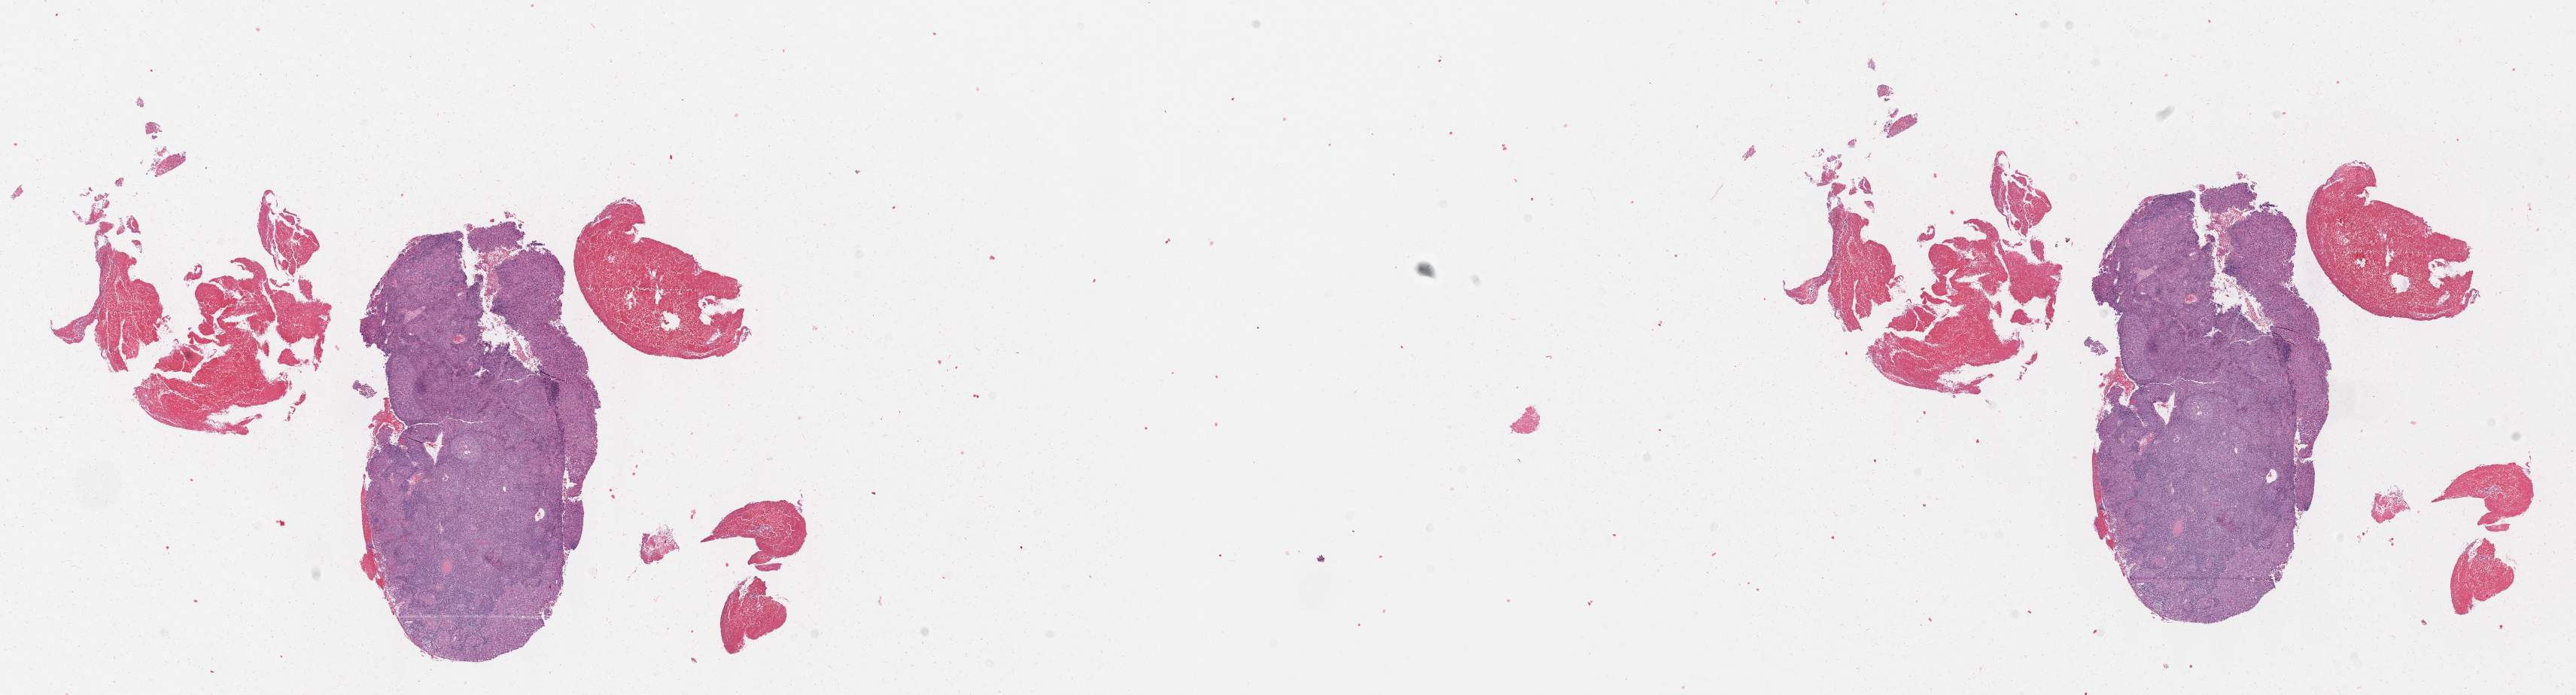
Hematoxylin and eosin (H&E) stained whole-slide image — whole scanned area (about 27.7 x 7.5 mm) shown as a low-resolution overview; formalin-fixed paraffin-embedded (FFPE) diagnostic section; cervix, primary tumour sample. Female, age 47 years at initial diagnosis. Histologic grade: G2 (moderately differentiated).
FIGO stage: IB2. Pathologic diagnosis: Squamous cell carcinoma, NOS (cervix uteri).